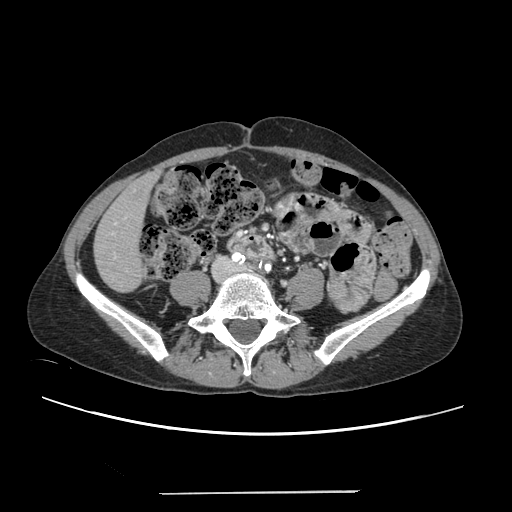
Contrast-enhanced abdominal CT, one axial slice; slice 35 of 240 in the series (ordered by position); intravenous contrast given; soft-tissue window (W 400 / L 40 HU); 1.25 mm slice thickness; 512 × 512 image matrix, field of view 371 × 371 mm. Female patient, age 60 years. From the clinical record (not read from this slice): diagnosis: colorectal cancer liver metastases, imaged before liver resection; multiple liver metastases: no; largest metastasis: 1.5 cm; disease in both lobes: no.
Outlined on this slice (outlined manually by an expert reader):
- liver: bounding box <95,175,155,292> (left, top, right, bottom; pixels)
- planned liver remnant (the part of the liver to remain after resection): <95,175,155,291>
- portal vein (with intrahepatic branches): <112,217,126,257>